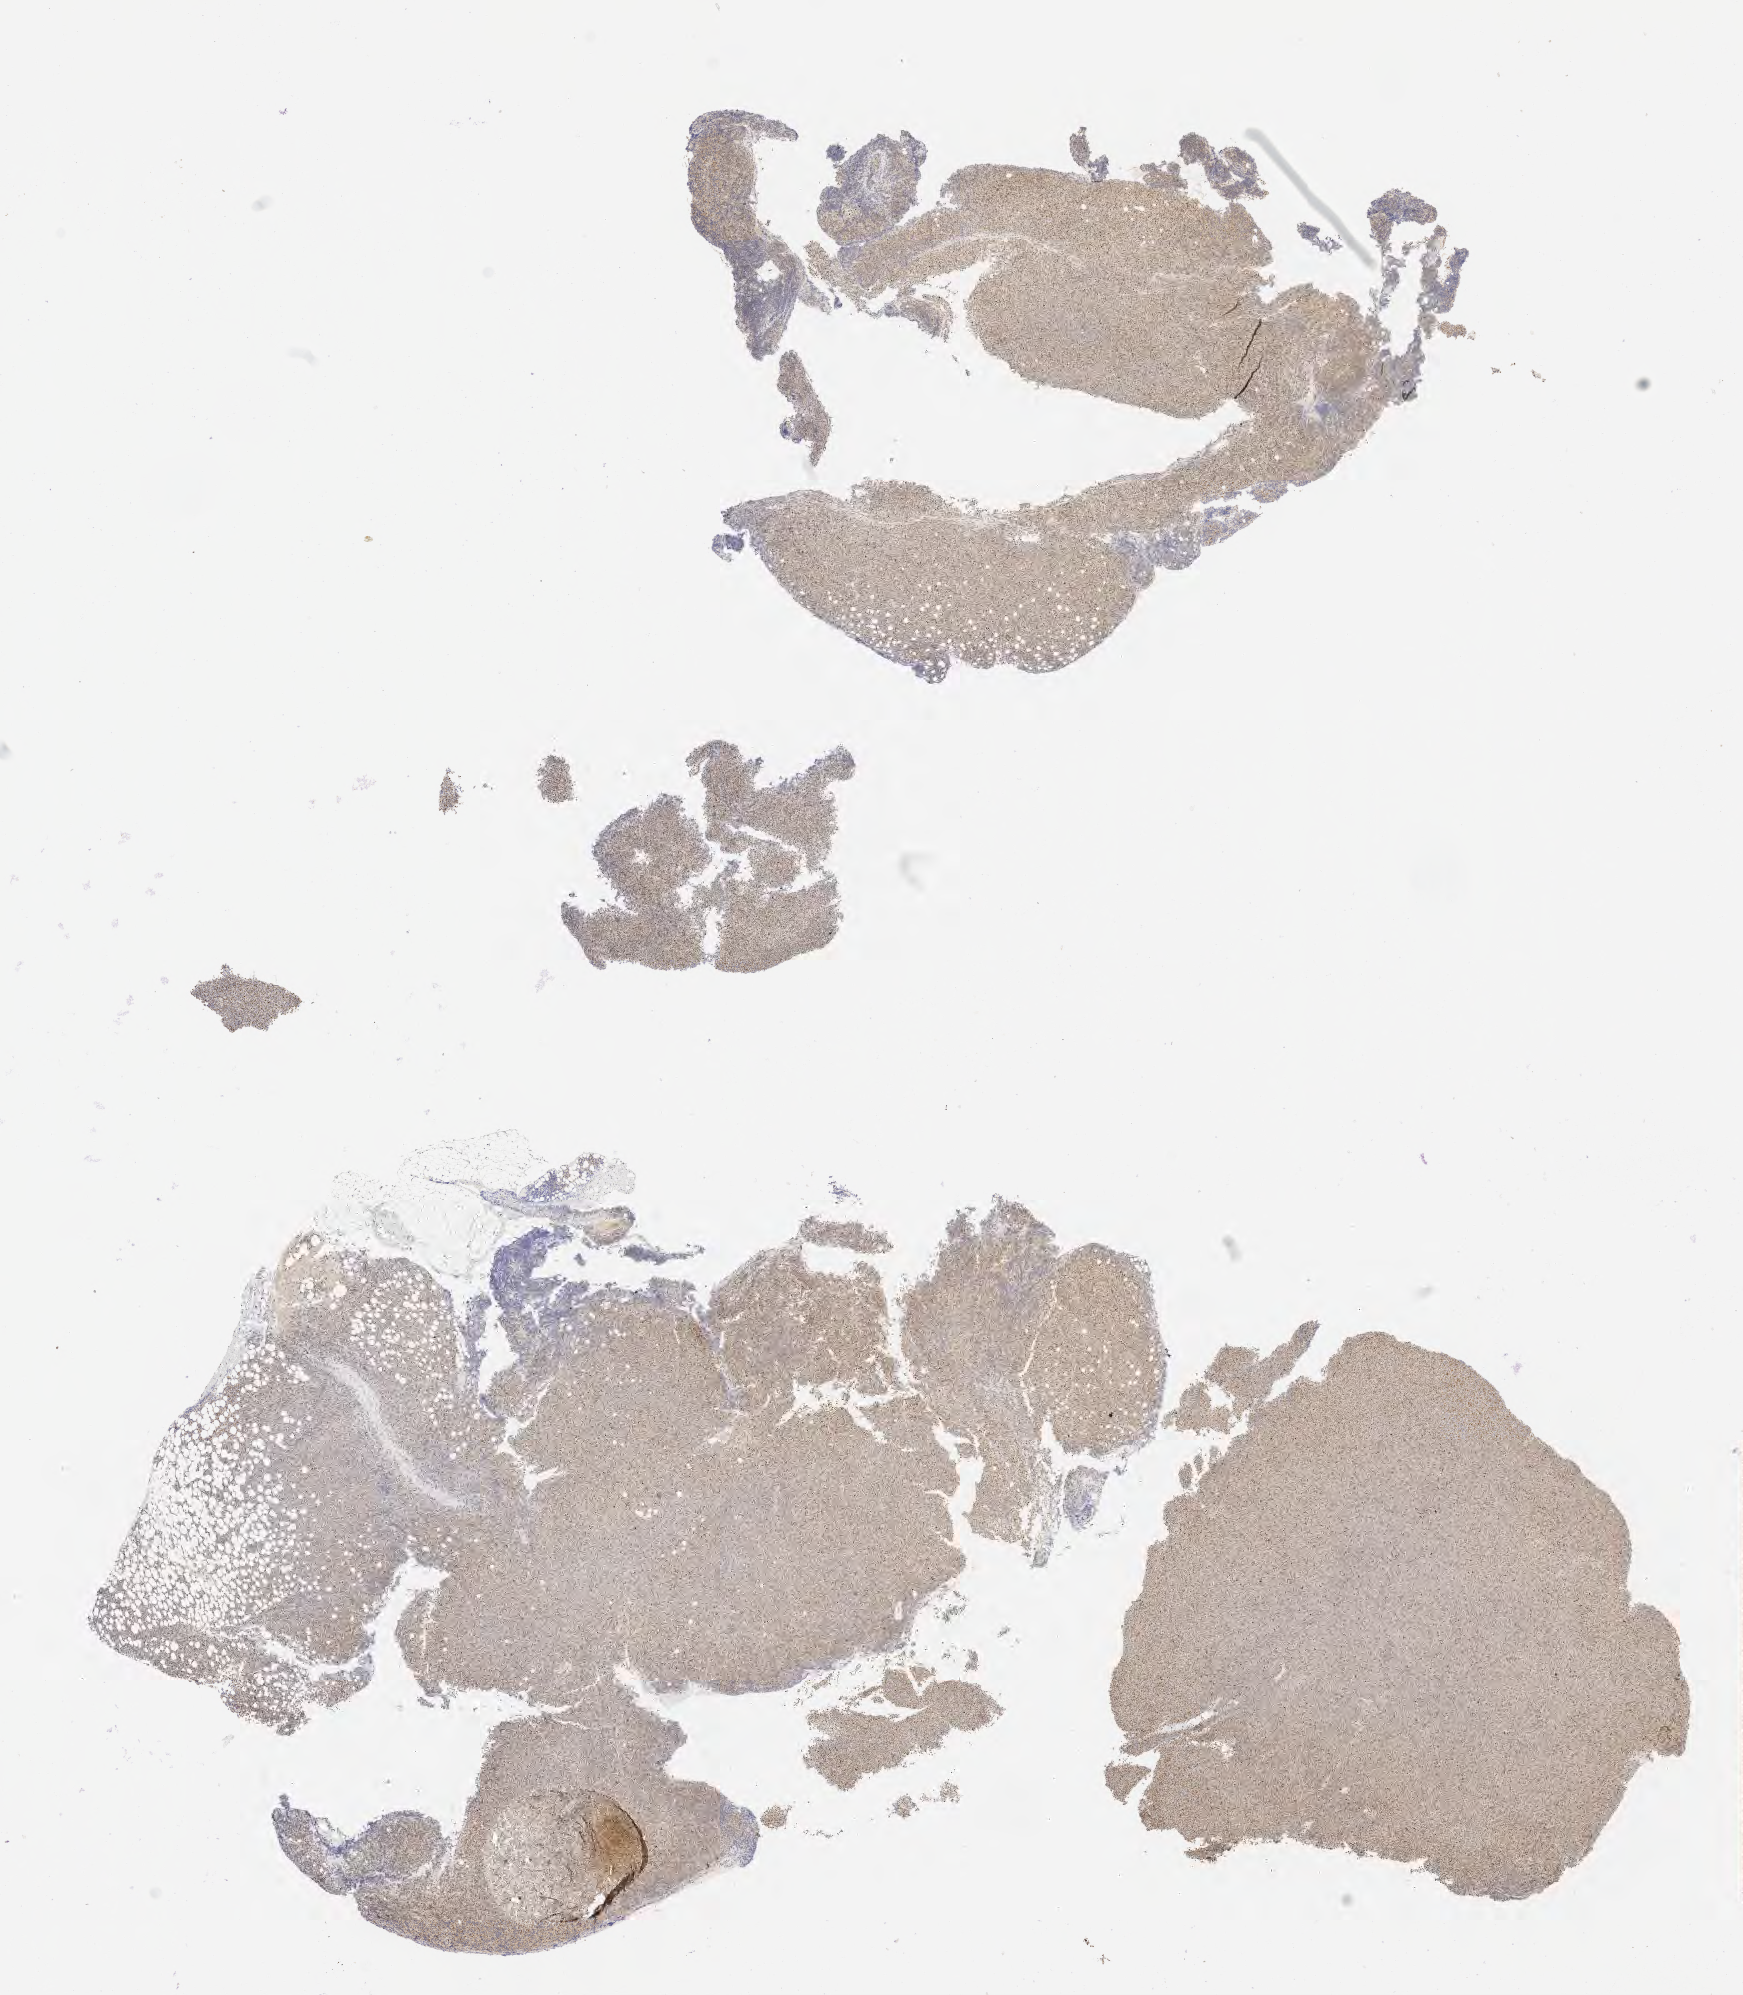
Immunohistochemistry (IHC) whole-slide image stained for p53 — a low-resolution overview of the entire scanned area, about 14.1 x 16.1 mm, specimen: tumor tissue. Female patient, 32 years old.
Diagnosis: Diffuse large B-cell lymphoma, NOS.